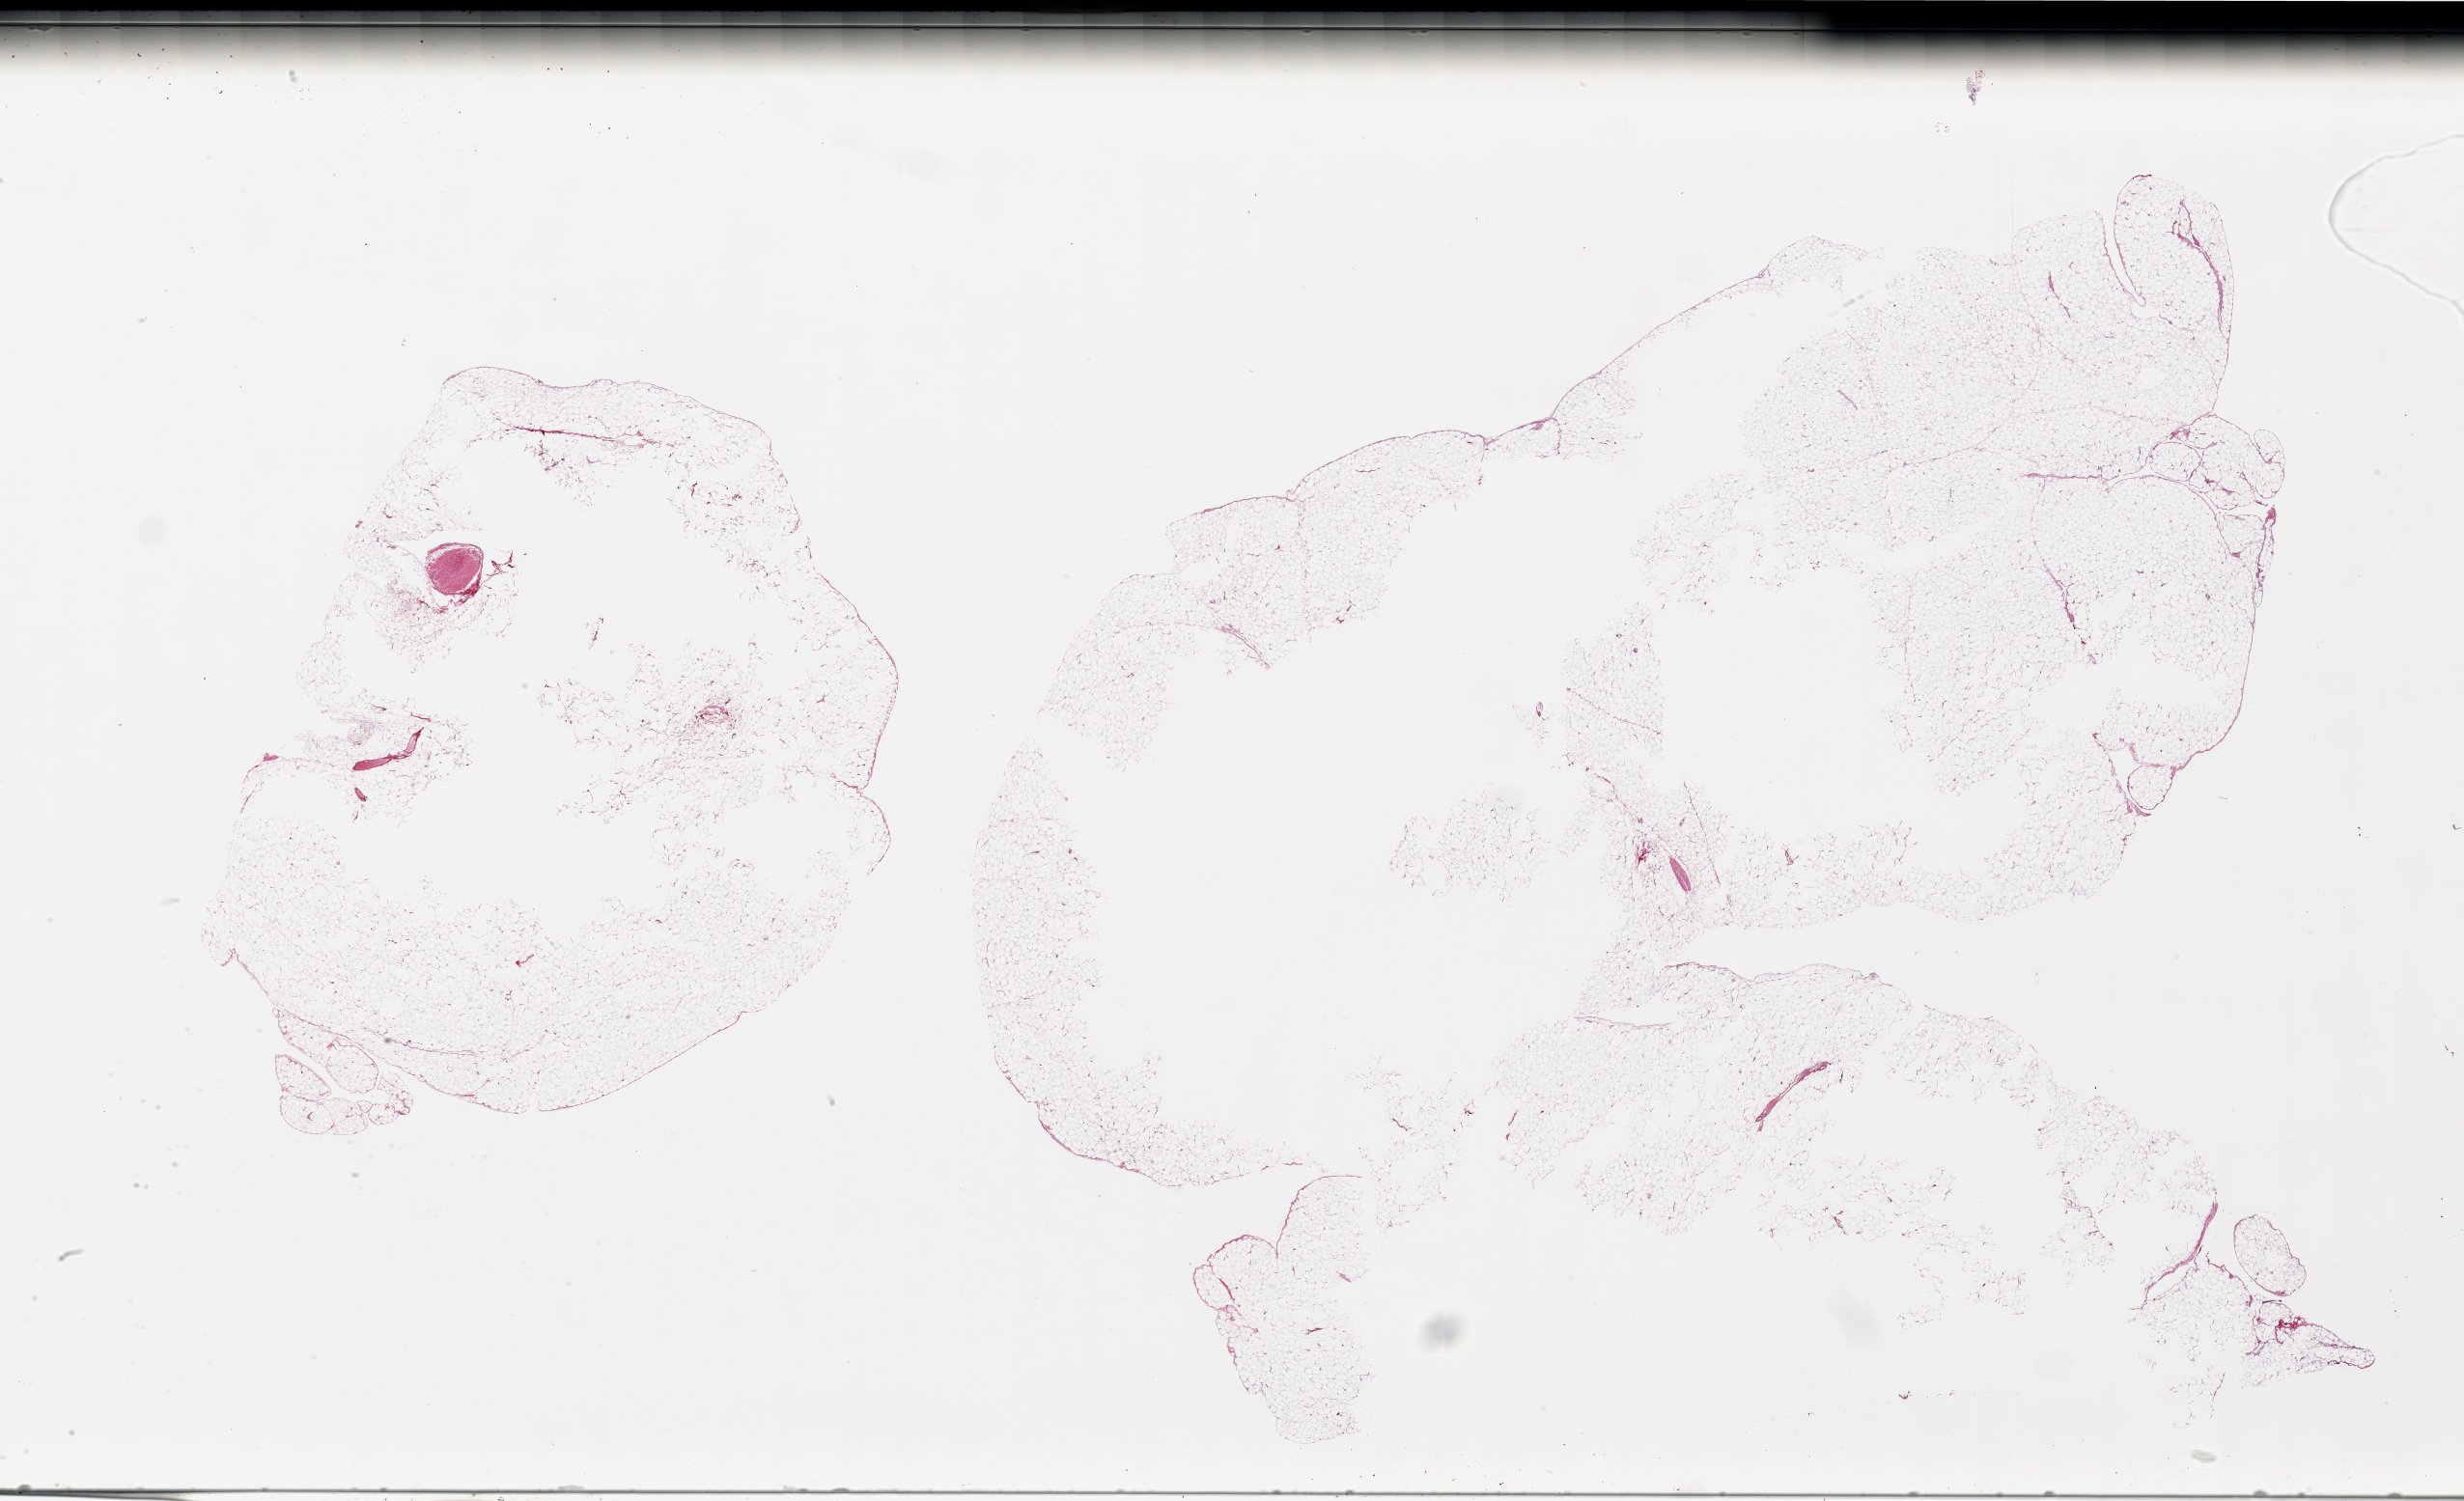
Digitized hematoxylin and eosin (H&E)-stained section, low-resolution overview of the scanned area, about 40.4 x 24.6 mm (from a 20x scan); PAXgene-fixed, paraffin-embedded tissue; sampled site (target tissue): omentum; donor tissue sample.
Reviewer comment on this tissue sample: 2 pieces; scattered empty spaces, possibly due to manual compression.